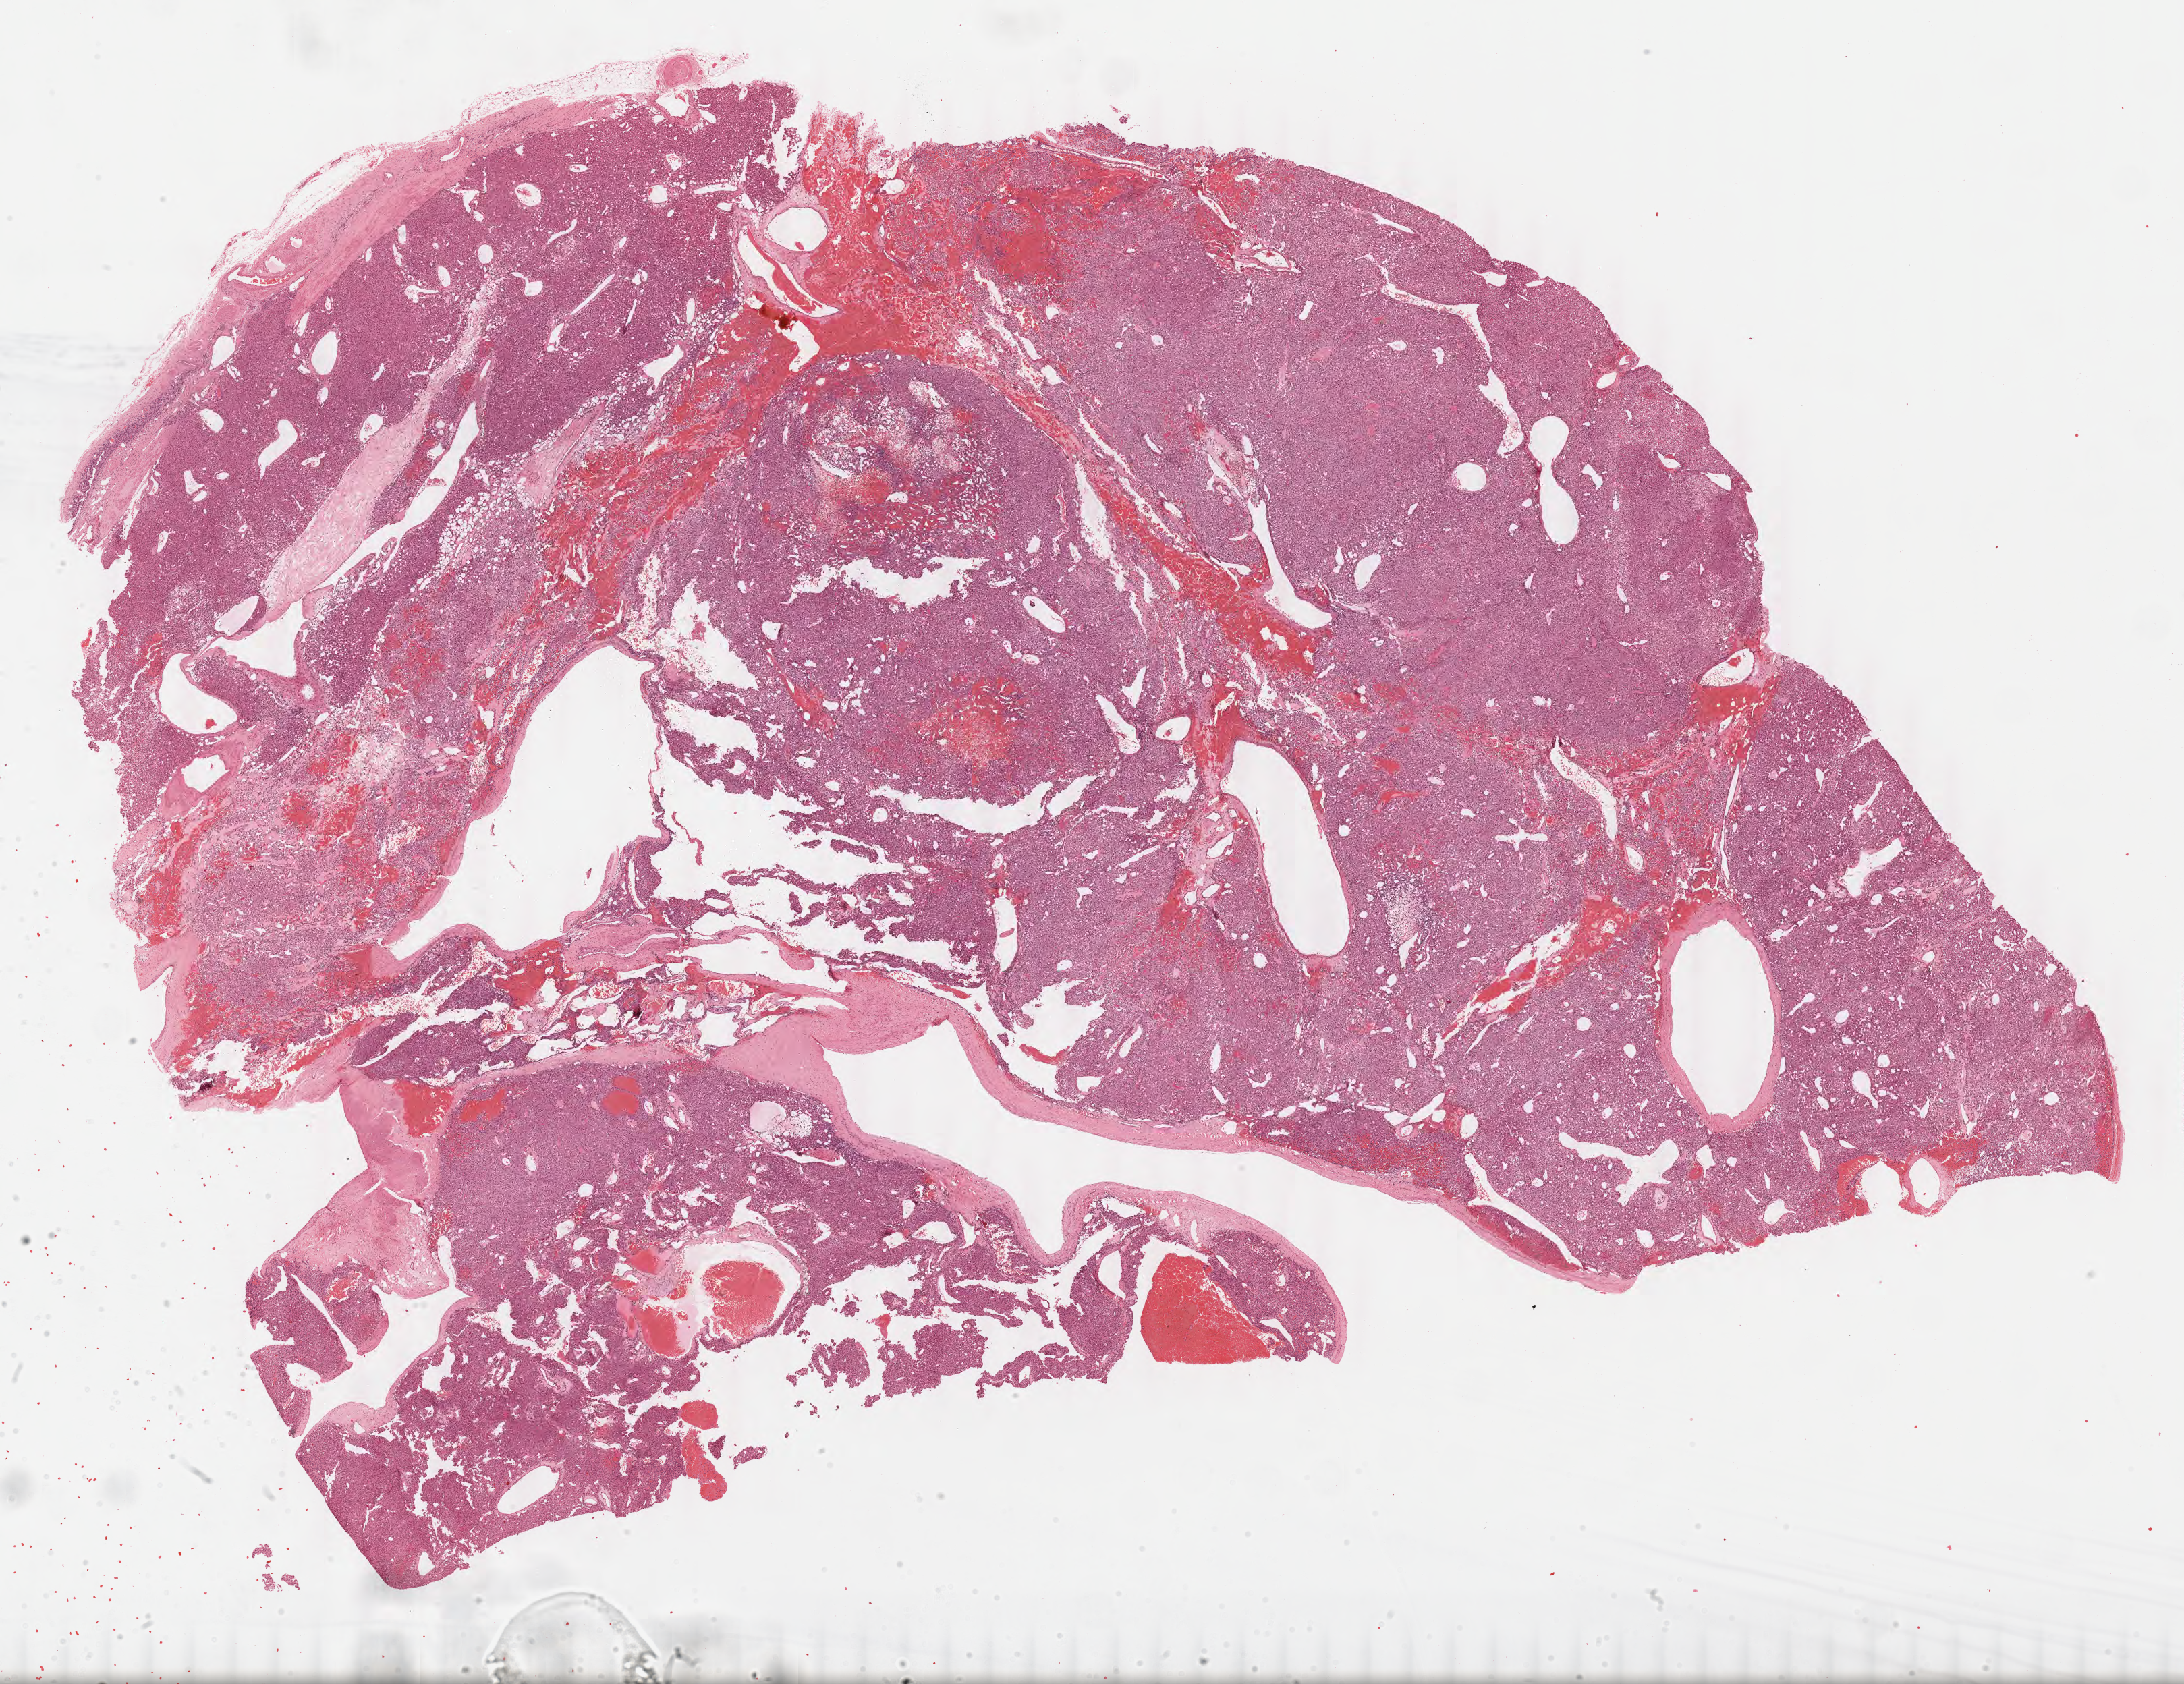
Whole-slide histology image, Hematoxylin and eosin (H&E) stained — low-resolution overview of the scanned area, about 25.6 x 19.7 mm; formalin-fixed paraffin-embedded (FFPE) diagnostic section; sample: primary tumour, adrenal cortex. Female, age 27 years at initial diagnosis.
Diagnosis: Adrenal cortical carcinoma (cortex of adrenal gland).